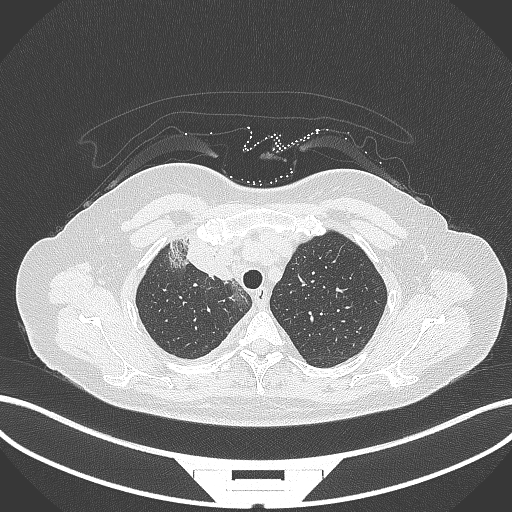
Chest CT, one axial slice. Position 250 of 305 along the scan axis. 120 kVp. Lung window (W 1500 / L -600 HU). 1 mm slice thickness. 512 × 512 image matrix. Patient: female, 52 years. Case-level facts recorded for this patient, not image findings: clinical TNM (as recorded): T3 N1 M1.
Structures marked on this image (rectangle marked by the reading radiologist):
- lung tumour (recorded histology: adenocarcinoma): bounding box [x1, y1, x2, y2] px = [167, 236, 235, 286]